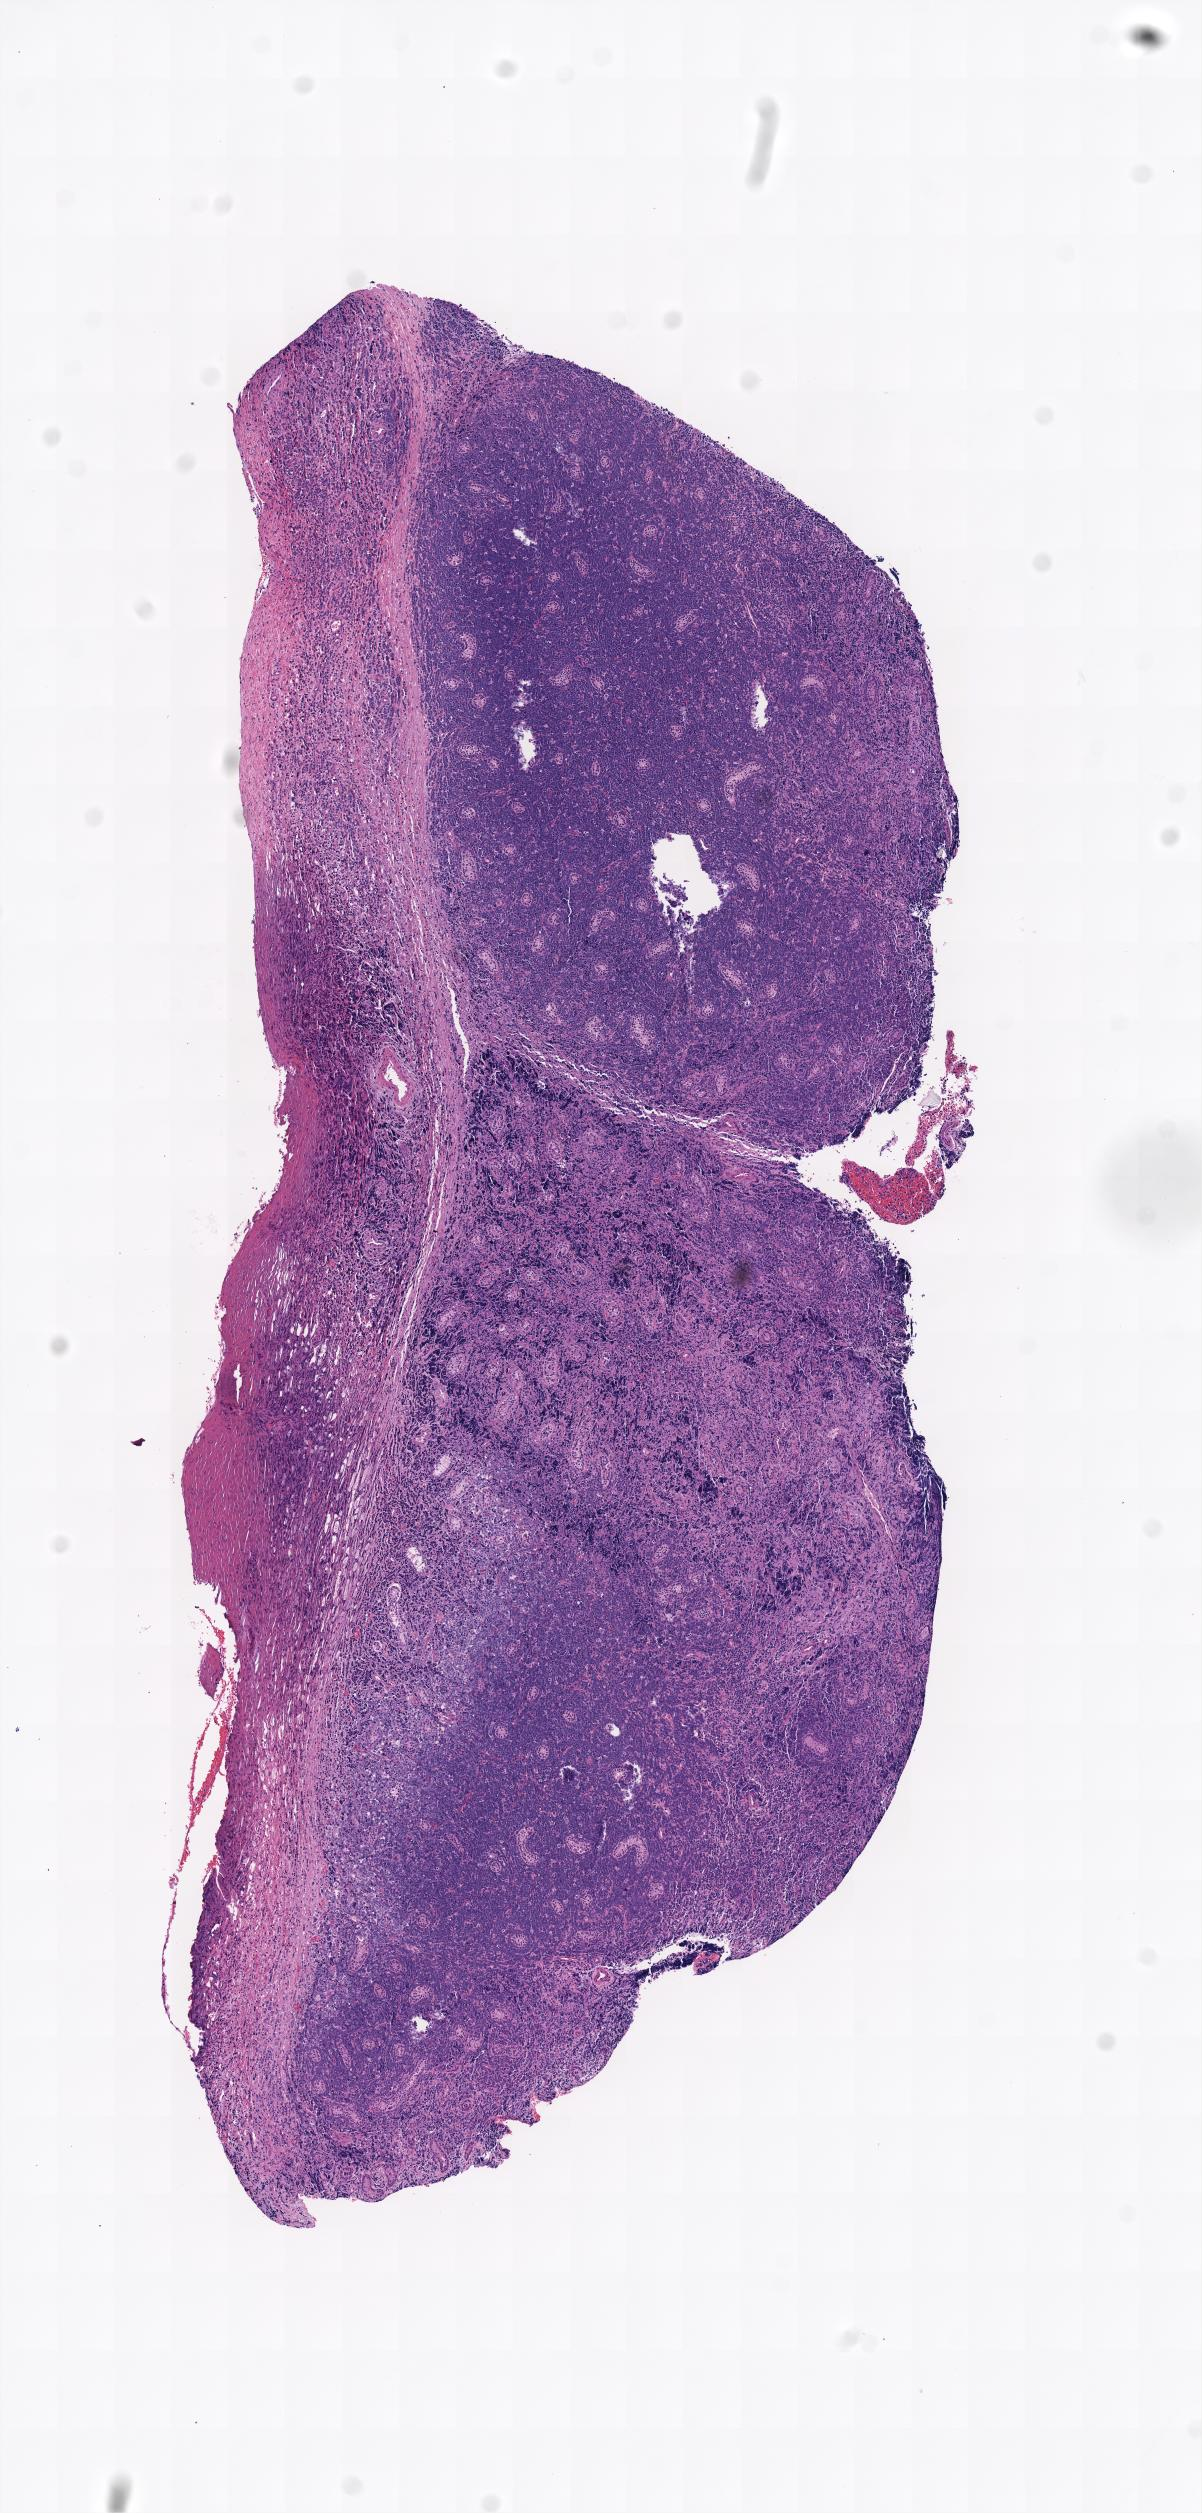
Digitized haematoxylin and eosin-stained section, a low-resolution overview of the entire scanned area. Tumor tissue. Site: testis. Male patient; age at initial diagnosis 8 years.
Histologic diagnosis: Burkitt lymphoma, NOS.